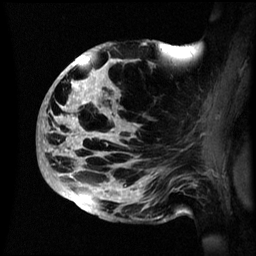
Breast MRI (dynamic contrast-enhanced), one sagittal slice. Position 33 of 60 along the scan axis. Dynamic contrast-enhanced series, image 2 of 3 at this slice position (ordered by acquisition). 1.5 T. TE 4.2 ms, TR 8.4 ms. 256 × 256 image matrix. Female patient, age 48 years.
Structures marked on this image (semi-automatically segmented with operator editing):
- analysis volume of interest (the breast-tissue region the enhancement analysis was run in; not a lesion): bounding box [x1, y1, x2, y2] px = [38, 41, 195, 222]
- tumour enhancement mask (voxels above the 70 % enhancement threshold inside the analysis volume of interest): [41, 56, 142, 213]